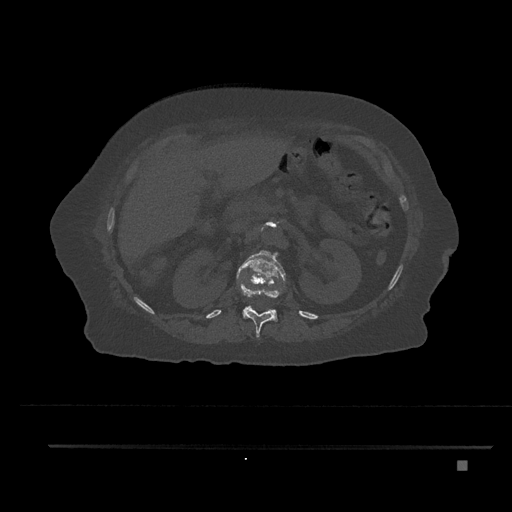
CT including the spine, one axial slice; slice 244 of 797 in the series (ordered by position); reconstruction kernel Br40s/3; 120 kVp; bone window (W 1800 / L 400 HU); 0.5 mm slice thickness; 512 × 512 image matrix, field of view 437 × 437 mm. Female patient, age 76 years. From the clinical record (not read from this slice): primary cancer: lung.
Outlined on this slice (semi-automatic segmentation, software-assisted and operator-edited):
- L1 vertebra: box from (x=237, y=250) to (x=286, y=321) px
- T12 vertebra: (x=240, y=280)–(x=280, y=337)